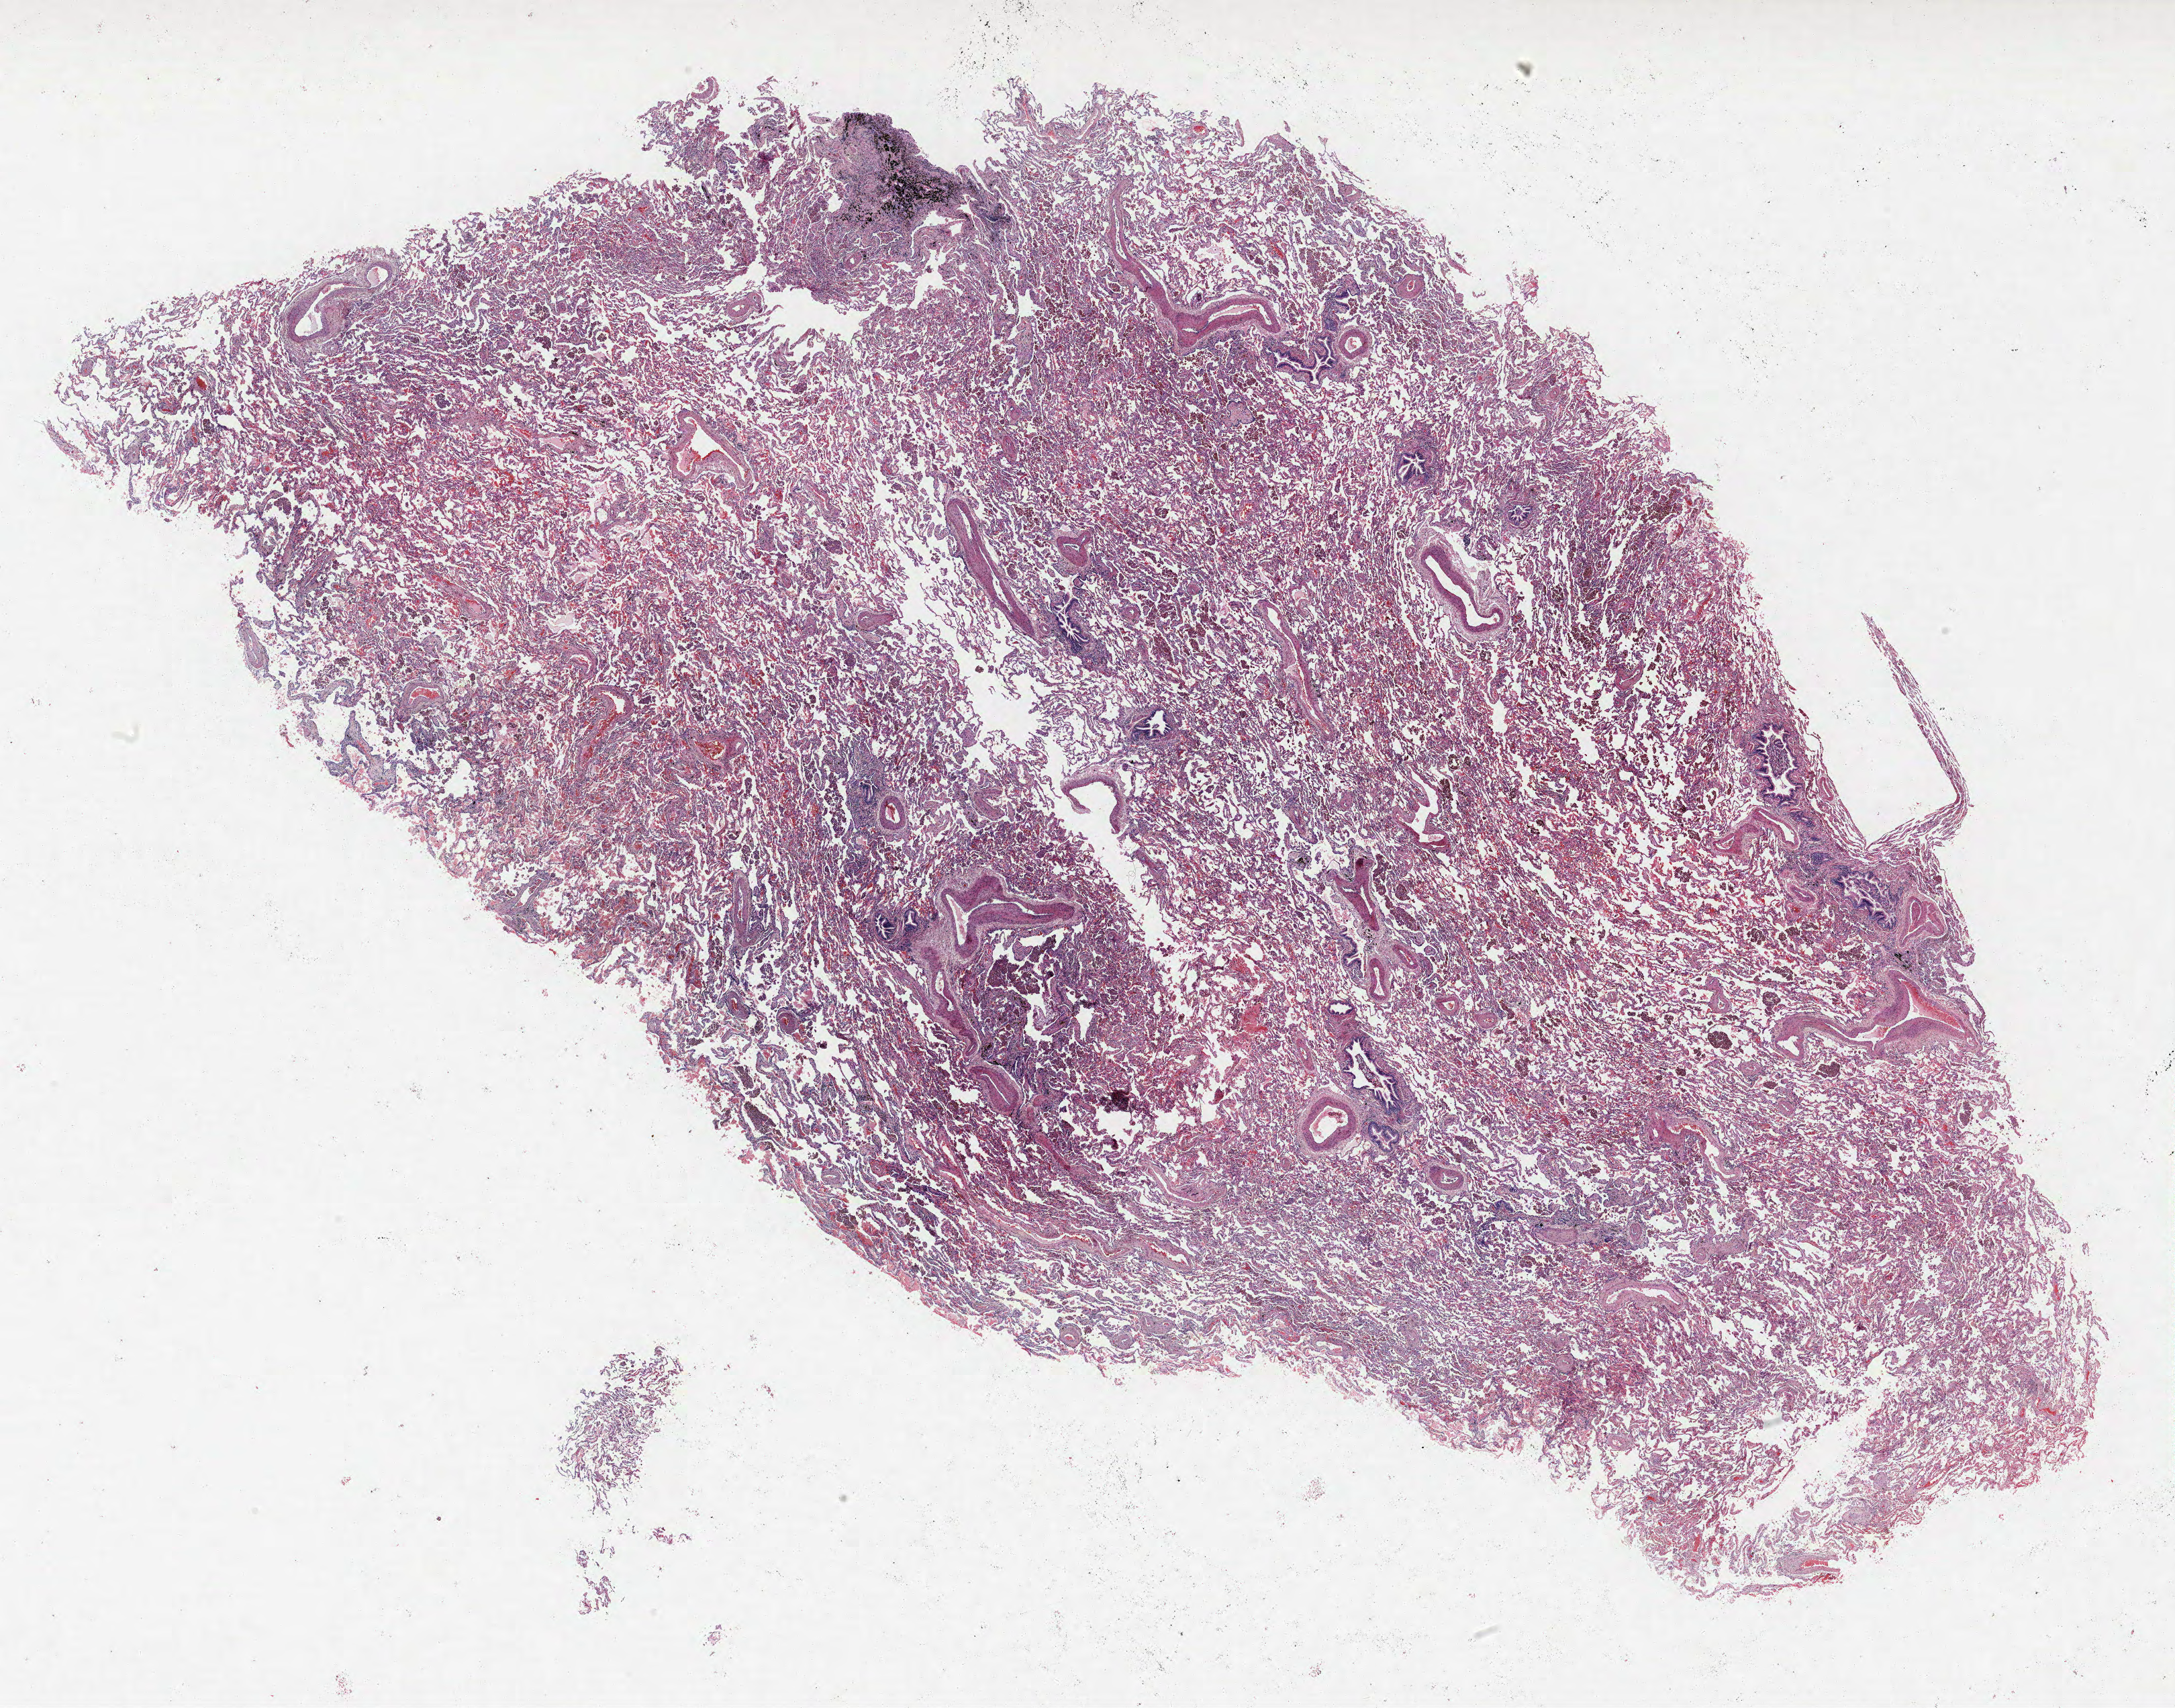
Whole-slide histology image, H&E-stained, whole scanned area (about 25.9 x 20.4 mm) shown as a low-resolution overview. FFPE section. Lung. Male patient, aged 63 at enrolment. Grade: poorly differentiated (G3).
Primary tumour location (clinical record): right lower lobe. Participant's lung-cancer diagnosis: Adenocarcinoma, NOS. Stage (AJCC 6th edition): IA. ICD-O-3 topography: lower lobe of lung (C34.3). Tumour size (pathology): 19 mm.